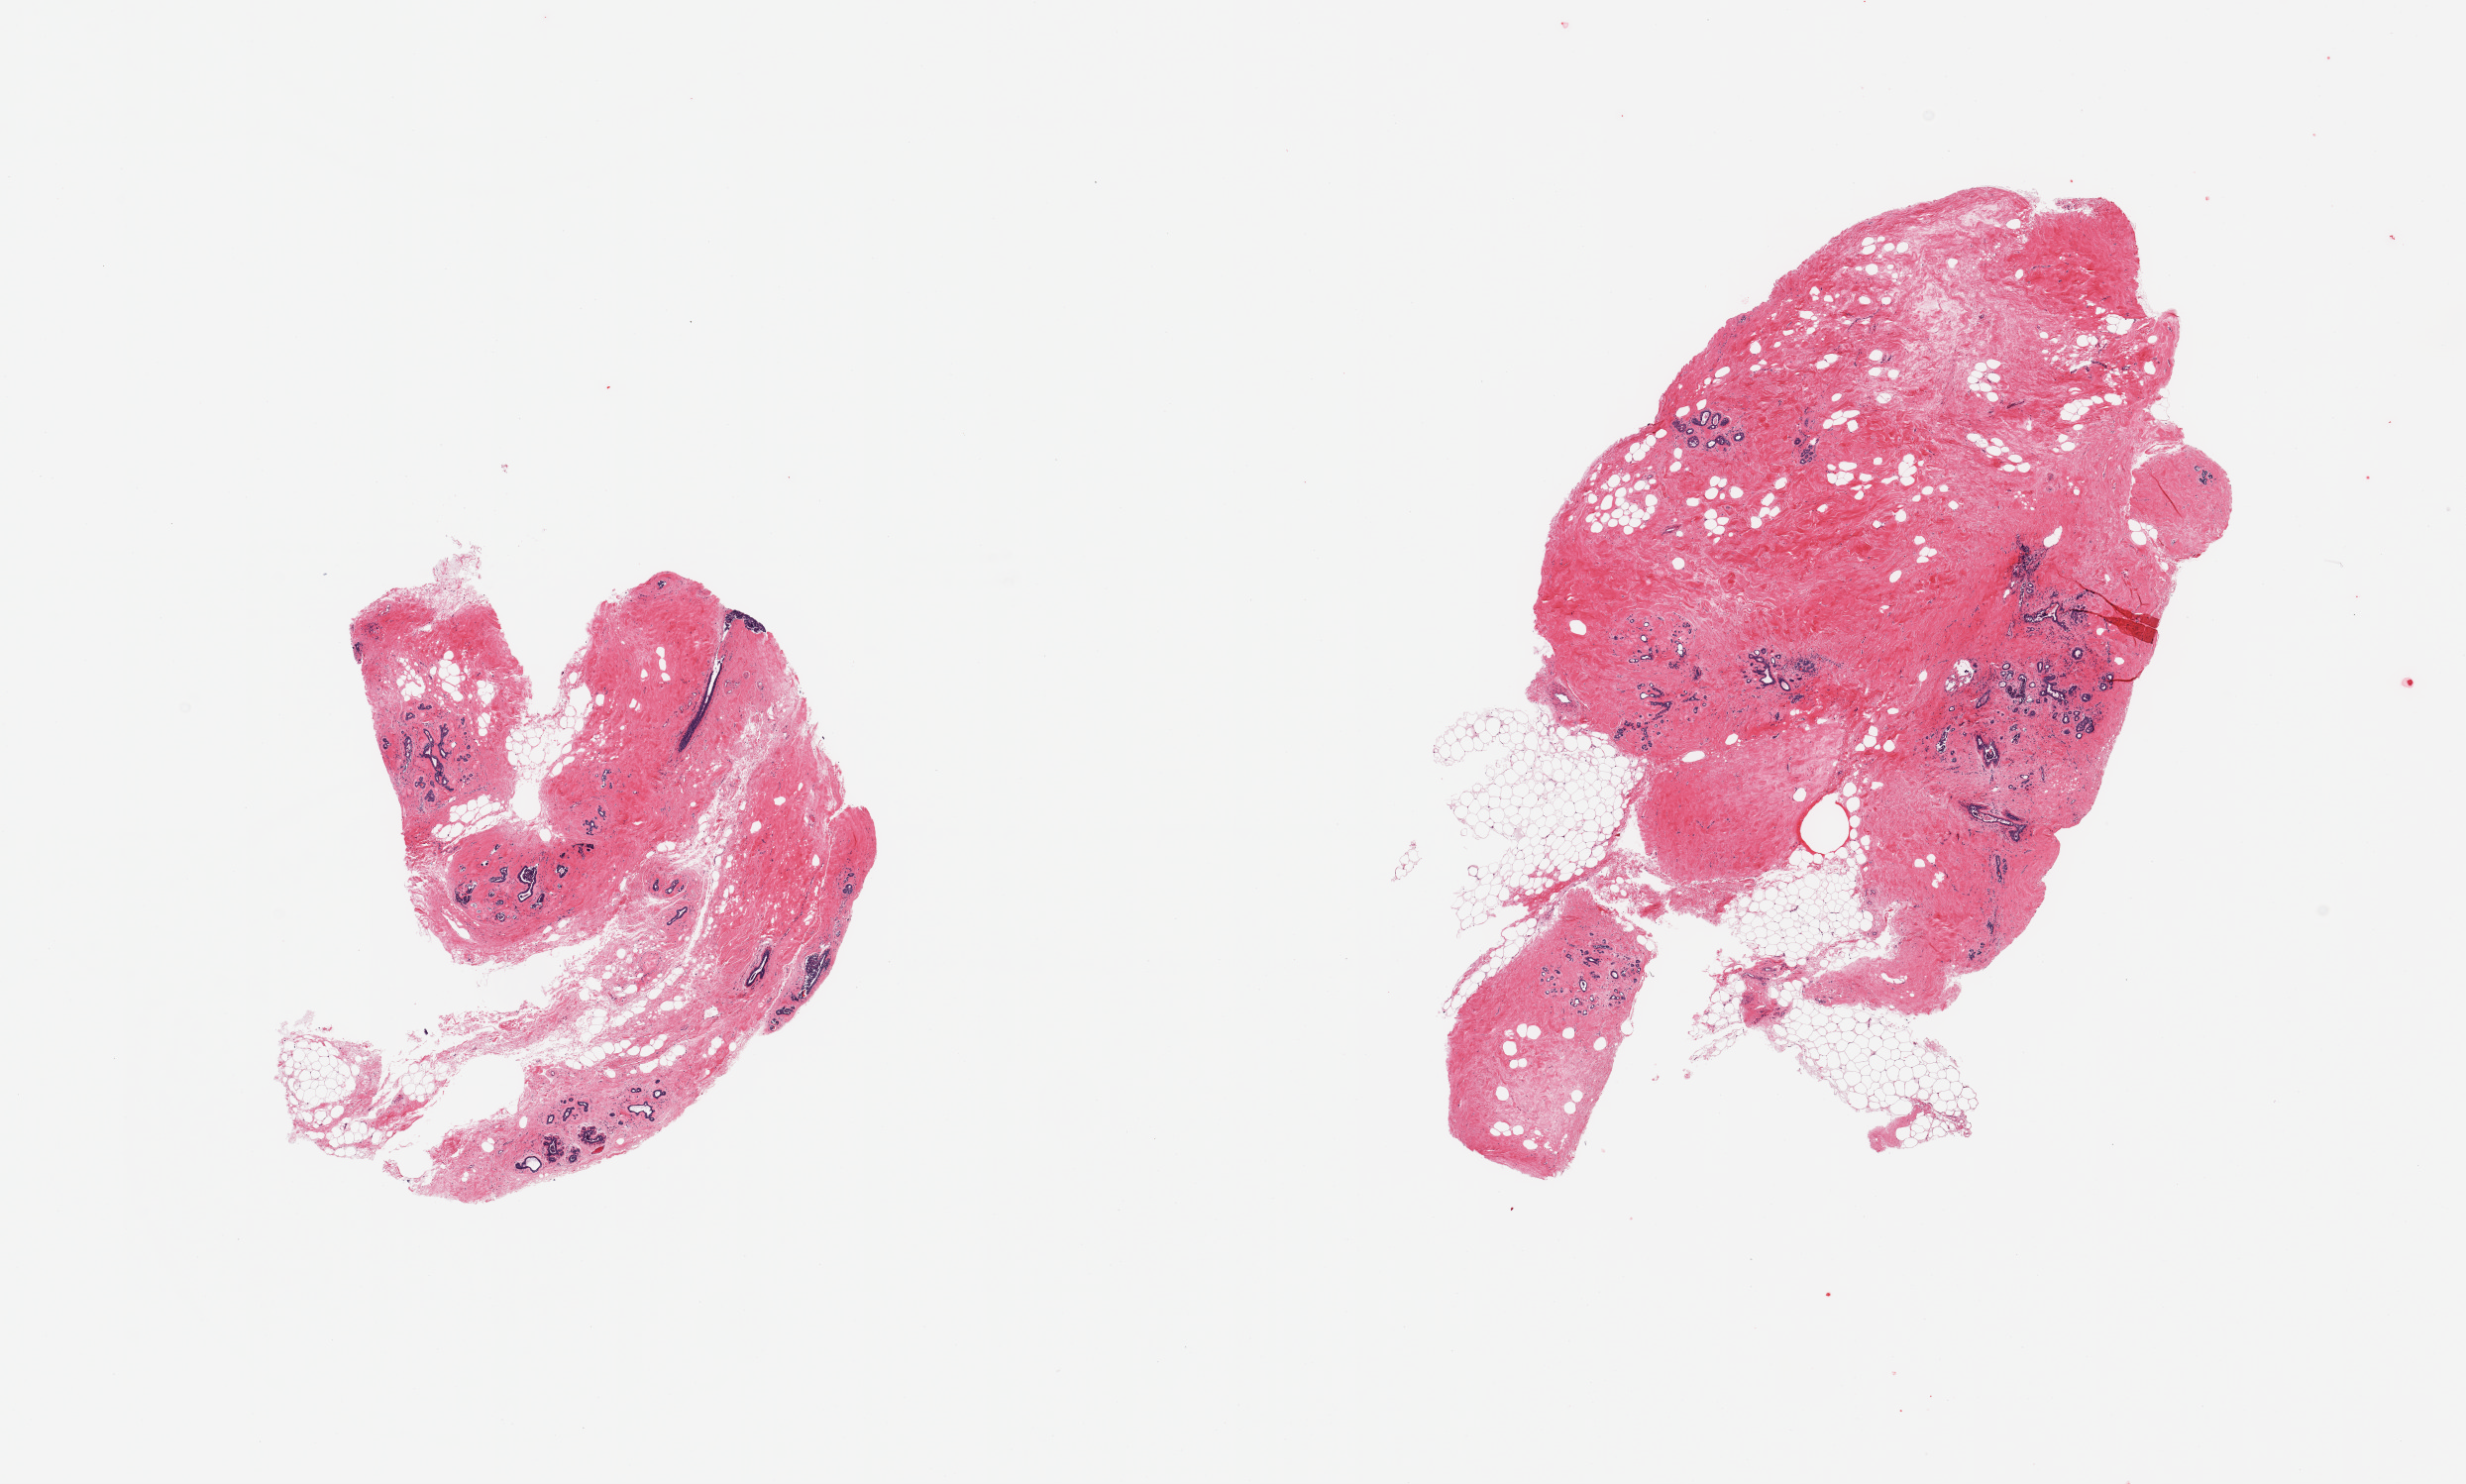
Whole-slide image, hematoxylin and eosin (H&E) stain — shown as a low-resolution overview of the whole scanned area (about 19.7 x 11.8 mm); PAXgene-fixed, paraffin-embedded tissue; section of breast (target tissue); donor tissue sample. Donor: female.
* reviewer comment on this tissue sample: 2 pieces, post menopausal atrophy; duct-lubular units; fibrous mastopathy